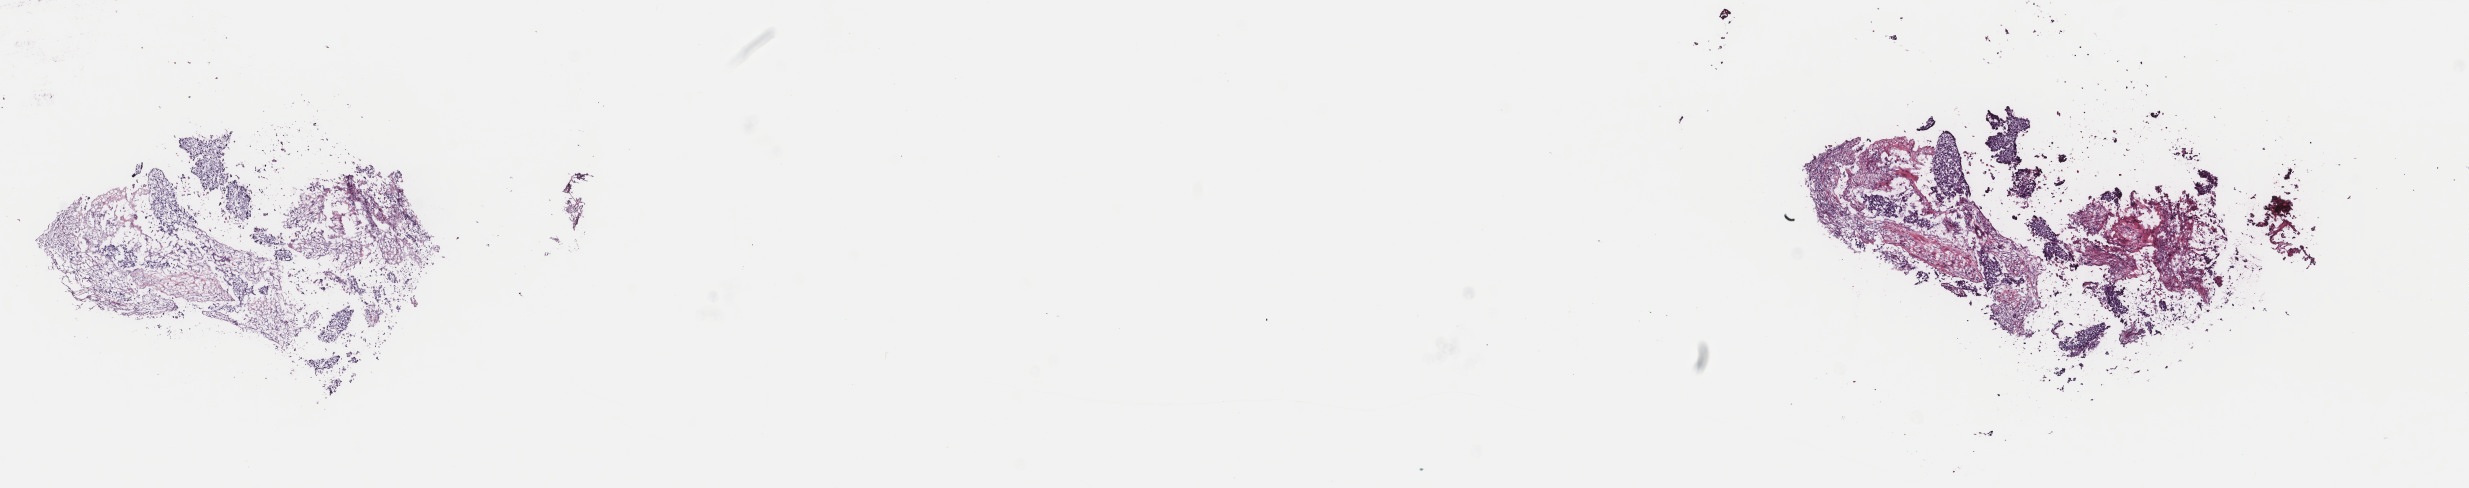
Whole-slide histology image, H&E — low-resolution overview of the scanned area, about 19.6 x 3.9 mm, frozen section from the top of the tissue portion, sample: primary tumour, bladder. Patient: male, age at initial diagnosis 76 years. Histologic grade: high grade. Composition of this section per pathologist review: tumour cells 75%, tumour nuclei 75%, normal cells 0%, stromal cells 25%, necrosis 0%. Inflammatory infiltration, as recorded: lymphocyte infiltration 5%, monocyte infiltration 1%, neutrophil infiltration 2%.
* lymph nodes positive (case pathology): 0 of 33 examined
* pathologic diagnosis: Transitional cell carcinoma (posterior wall of bladder)
* AJCC pathologic stage: III (7th edition)
* TNM: T3a N0 MX